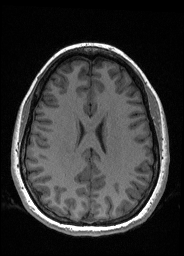
Pre-operative brain MRI before brain-tumour surgery, one axial slice; slice 73 of 176 in the series (ordered by position); T1-weighted post-contrast; 1 mm slice thickness; 184 × 256 image matrix, field of view 180 × 250 mm. From the clinical record (not read from this slice): histopathology: Oligodendroglioma; WHO grade: 2; IDH mutation: yes.
Annotated regions visible in this slice (expert manual segmentation):
- tumour: bounding box (x1, y1, x2, y2) in pixels: (100, 113, 106, 120)